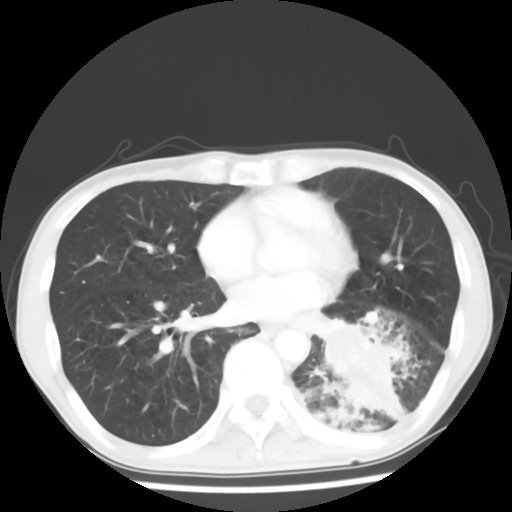
Chest CT, one axial slice; position 26 of 64 along the scan axis; lung window (W 1500 / L -600 HU); 5 mm slice thickness; 512 × 512 image matrix. Male patient, age 68 years. Case-level facts recorded for this patient, not image findings: clinical TNM (as recorded): T4 N0 M0.
Outlined on this slice (rectangle marked by the reading radiologist):
- lung tumour (recorded histology: squamous cell carcinoma): bounding box <307,312,378,371> (left, top, right, bottom; pixels)